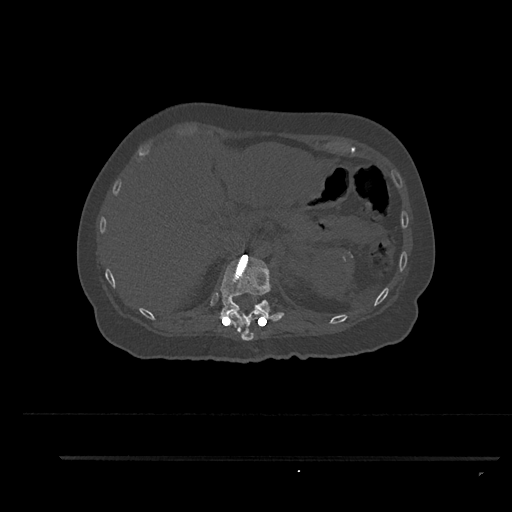
CT including the spine, one axial slice. Position 285 of 797 along the scan axis. Reconstruction kernel Br40s/3. Bone window (W 1800 / L 400 HU). 0.5 mm slice thickness. 512 × 512 image matrix. Female patient, age 44 years. From the clinical record (not read from this slice): primary cancer: renal; vertebrae with lytic lesions (as recorded): L1.
Structures marked on this image (semi-automatic segmentation, software-assisted and operator-edited):
- T11 vertebra: bounding box [x1, y1, x2, y2] px = [232, 309, 264, 341]
- T12 vertebra: [220, 249, 283, 322]